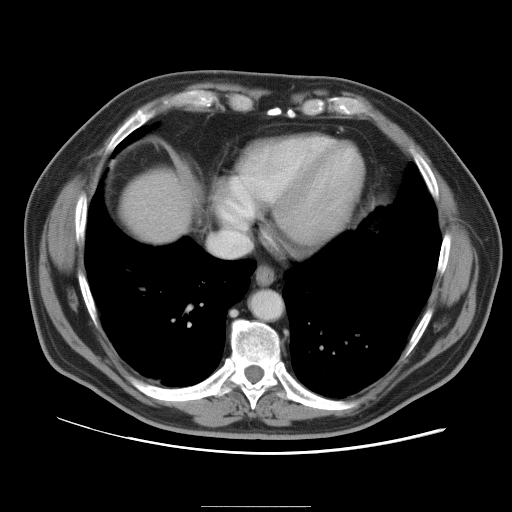
Contrast-enhanced abdominal CT, one axial slice. Slice 94 of 105 in the series (ordered by position). Soft-tissue window (W 400 / L 40 HU). 512 × 512 image matrix, field of view 399 × 399 mm. Male patient, age 64 years. Case-level facts recorded for this patient, not image findings: diagnosis: colorectal cancer liver metastases, imaged before liver resection; multiple liver metastases: yes; largest metastasis: 3 cm; chemotherapy before resection: yes.
Outlined on this slice (outlined manually by an expert reader):
- liver: box from (x=121, y=172) to (x=190, y=243) px
- planned liver remnant (the part of the liver to remain after resection): (x=123, y=174)–(x=191, y=243)